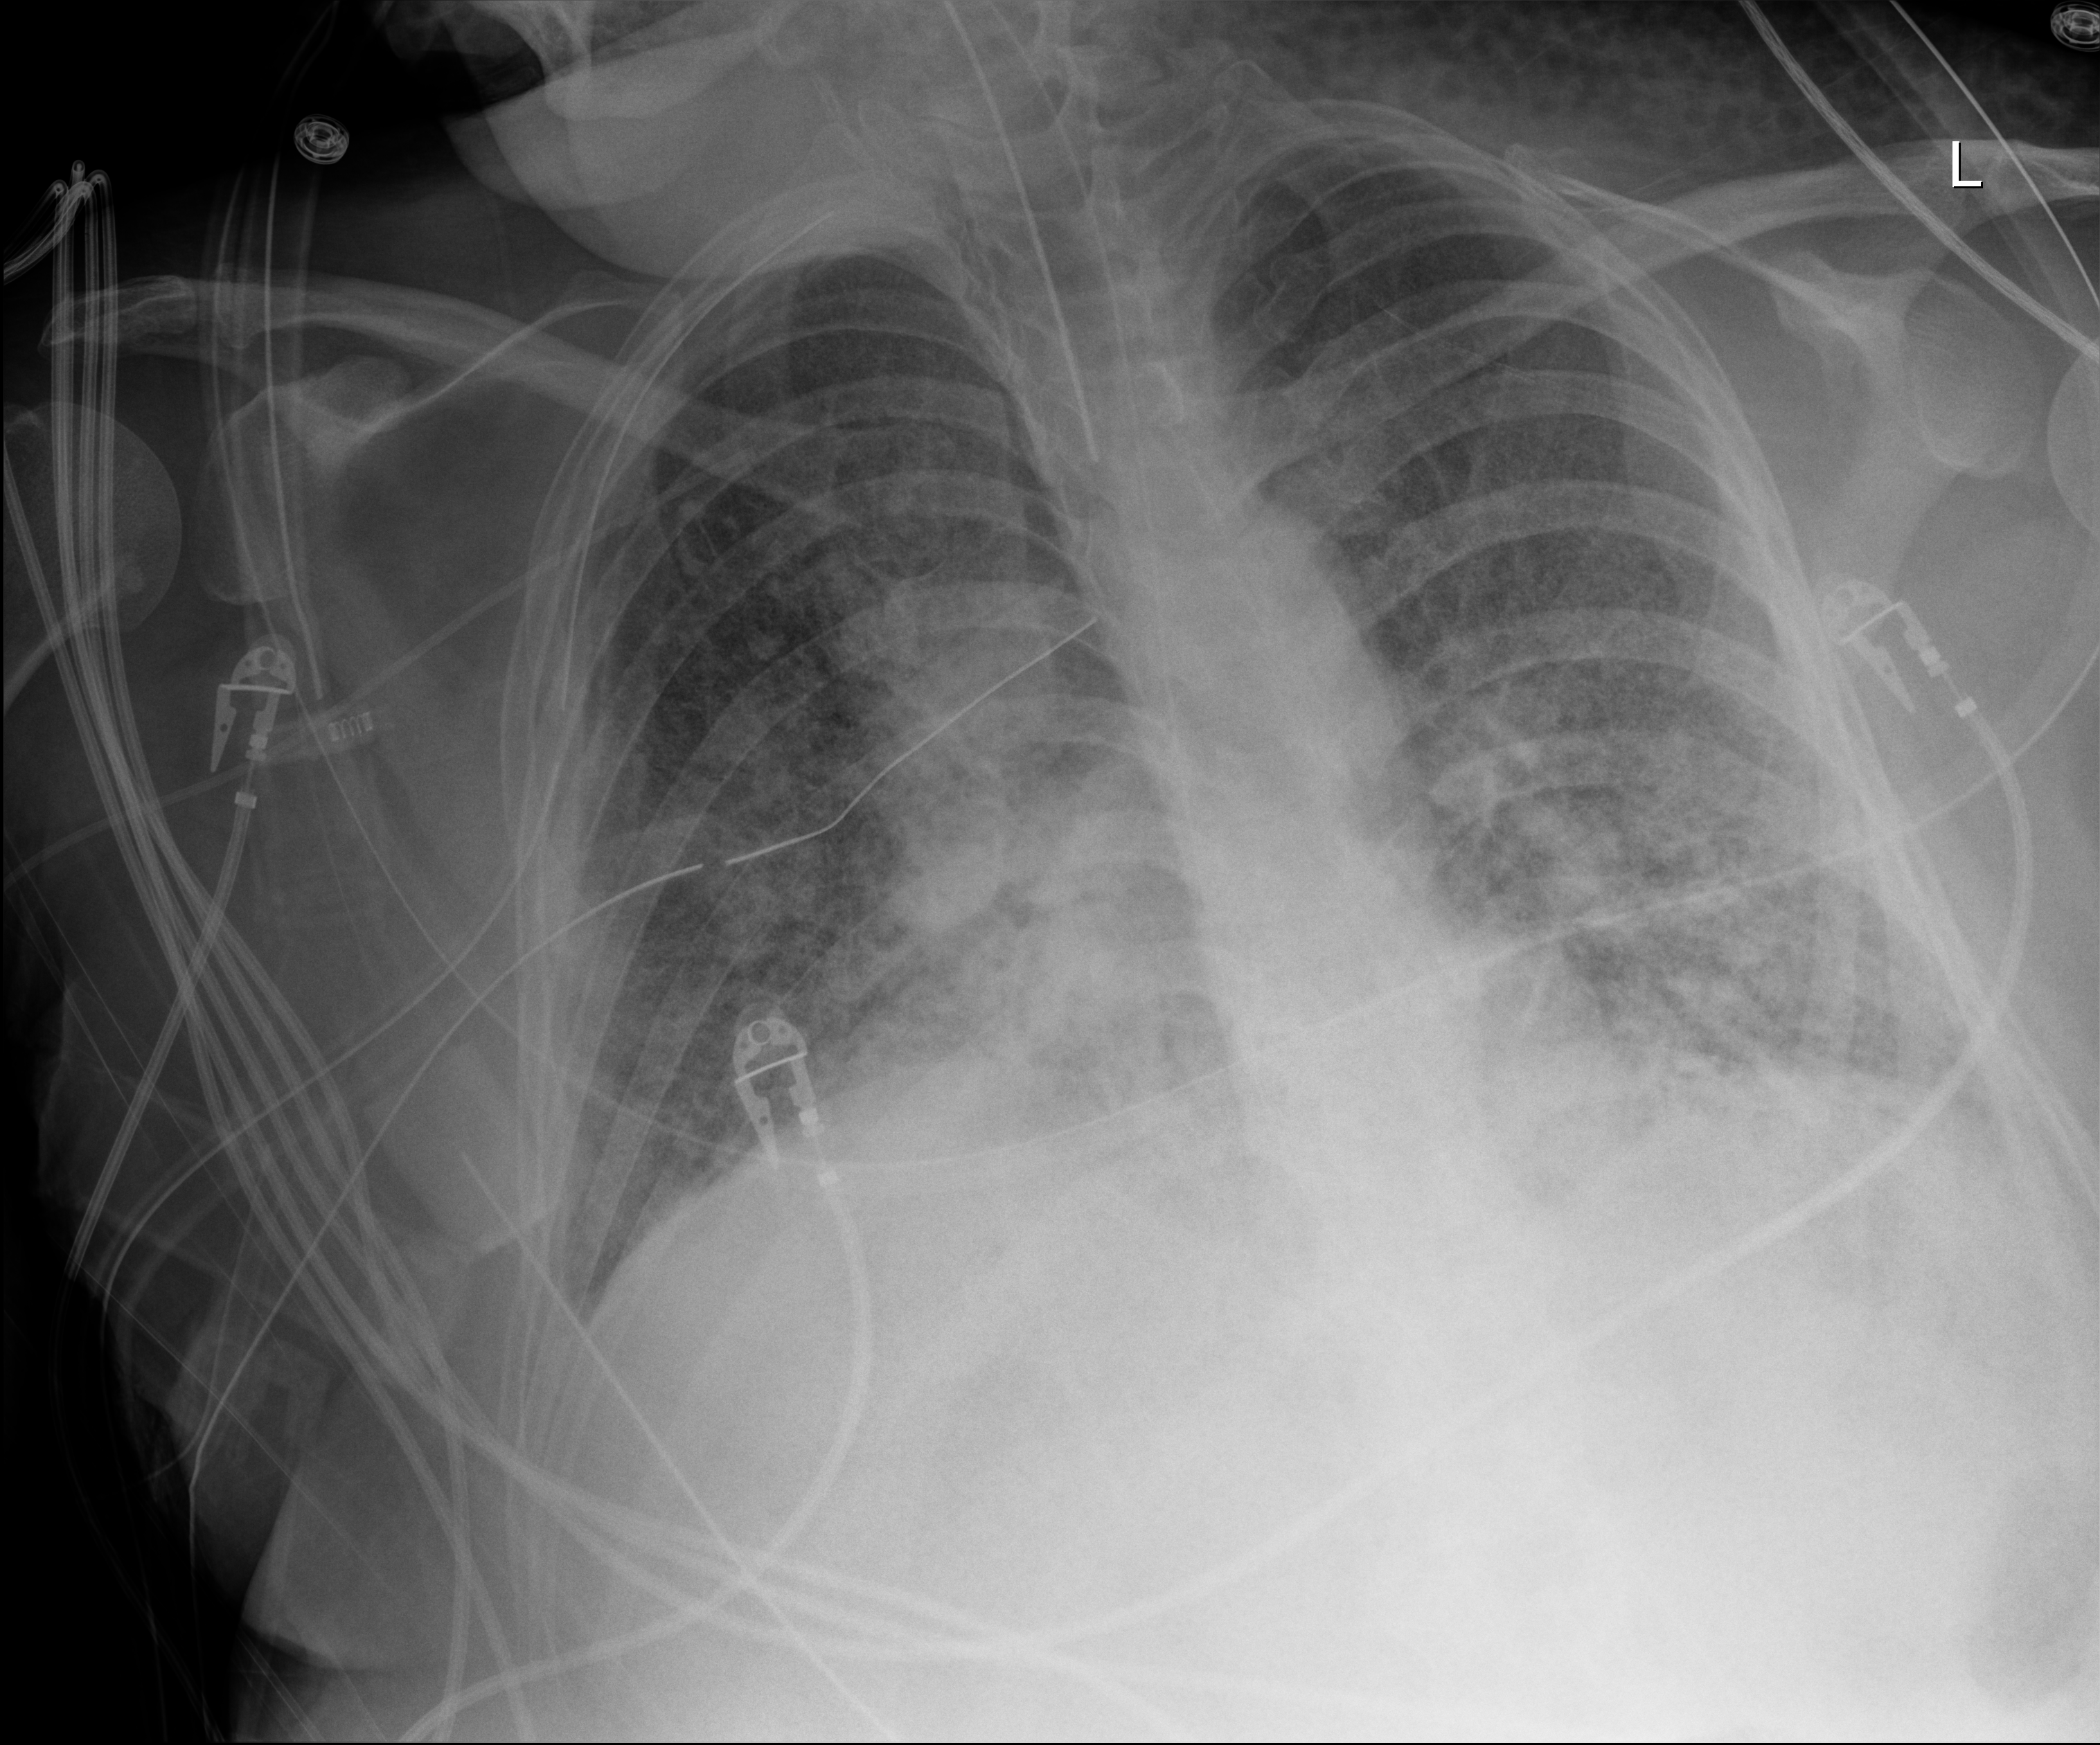
Bedside chest radiograph (digital radiography); anteroposterior (AP) projection. Patient hospitalised with COVID-19, aged 18–59 years.
Admission-level facts for this patient (not findings on this image; timing relative to this image not recorded):
- admitted to intensive care during this hospital stay: yes